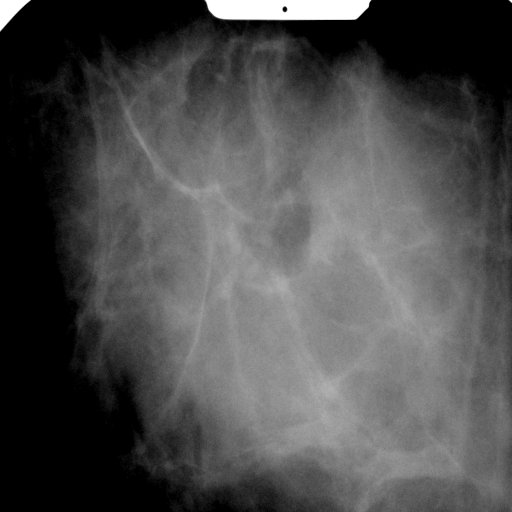
Spot-compression mammographic view.
Pathology recorded for this patient (not read from this image): pathology diagnosis: benign fibroadenoma (right breast); pathology report notes: RIGHT BREAST CALCIFICATION WITH NEEDLE LOCATION: FIBROADENOMA (1.9CM). REMAINING BREAST TISSUE WITH ADENOSIS, FOCAL FIBROADENOMATOUS CHANGES, APOCRINE METAPLASIA, FIBROCYSTIC CHANGES, SMALL INTRADUCTAL PAPILLOMAS, AND USUAL TYPE DUCTAL HYPERPLASIA. MICROCALCIFICATIONS ASSOCIATED WITH BENIGN BREAST TISSUE ARE IDENTIFIED. NO IN-SITU OR INVASIVE CARCINOMA.